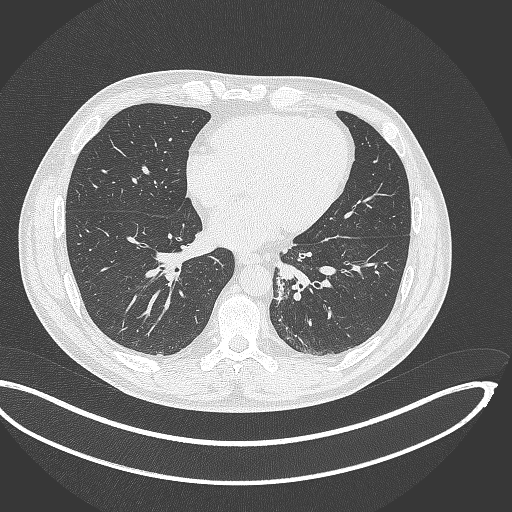
Chest CT, one axial slice. Reconstruction kernel B70f. Lung window (W 1500 / L -600 HU). 1 mm slice thickness. 512 × 512 image matrix, field of view 442 × 442 mm. Patient: male, 50 years. From the clinical record (not read from this slice): clinical TNM (as recorded): T2a N3 M0.
Annotated regions visible in this slice (rectangle marked by the reading radiologist):
- lung tumour (recorded histology: squamous cell carcinoma): bounding box (x1, y1, x2, y2) in pixels: (269, 273, 291, 306)